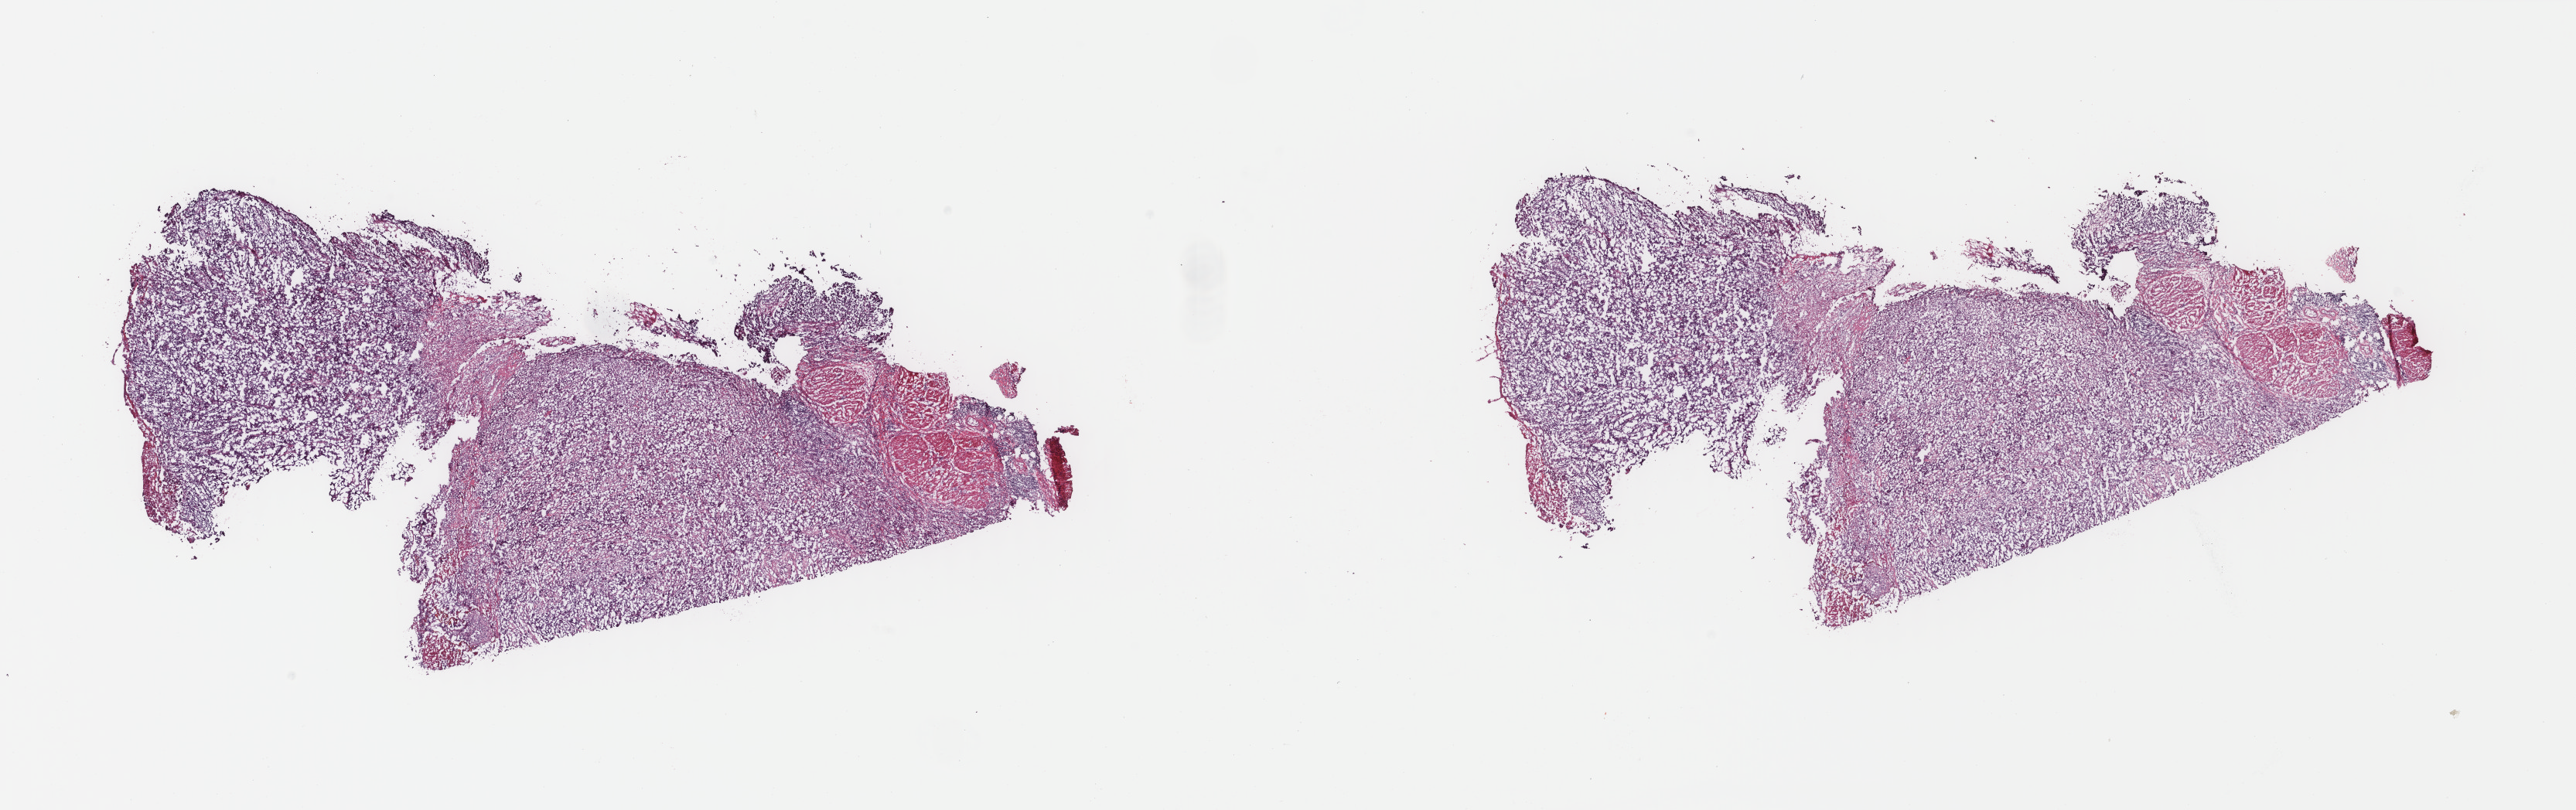
Whole-slide histology image, H&E-stained — whole scanned area (about 26.4 x 8.3 mm) shown as a low-resolution overview, frozen section from the top of the tissue portion, sample: primary tumour, bladder. Male, age 75 years at initial diagnosis. Histologic grade: high grade. Composition of this section per pathologist review: tumour cells 70%, tumour nuclei 75%, normal cells 0%, stromal cells 25%, necrosis 5%. Inflammatory infiltration, as recorded: lymphocyte infiltration 8%, monocyte infiltration 0%, neutrophil infiltration 0%.
TNM: T2b N0 MX. Pathologic diagnosis: Papillary transitional cell carcinoma. Lymph nodes positive (case pathology): 0 of 15 examined. AJCC pathologic stage: II (7th edition).